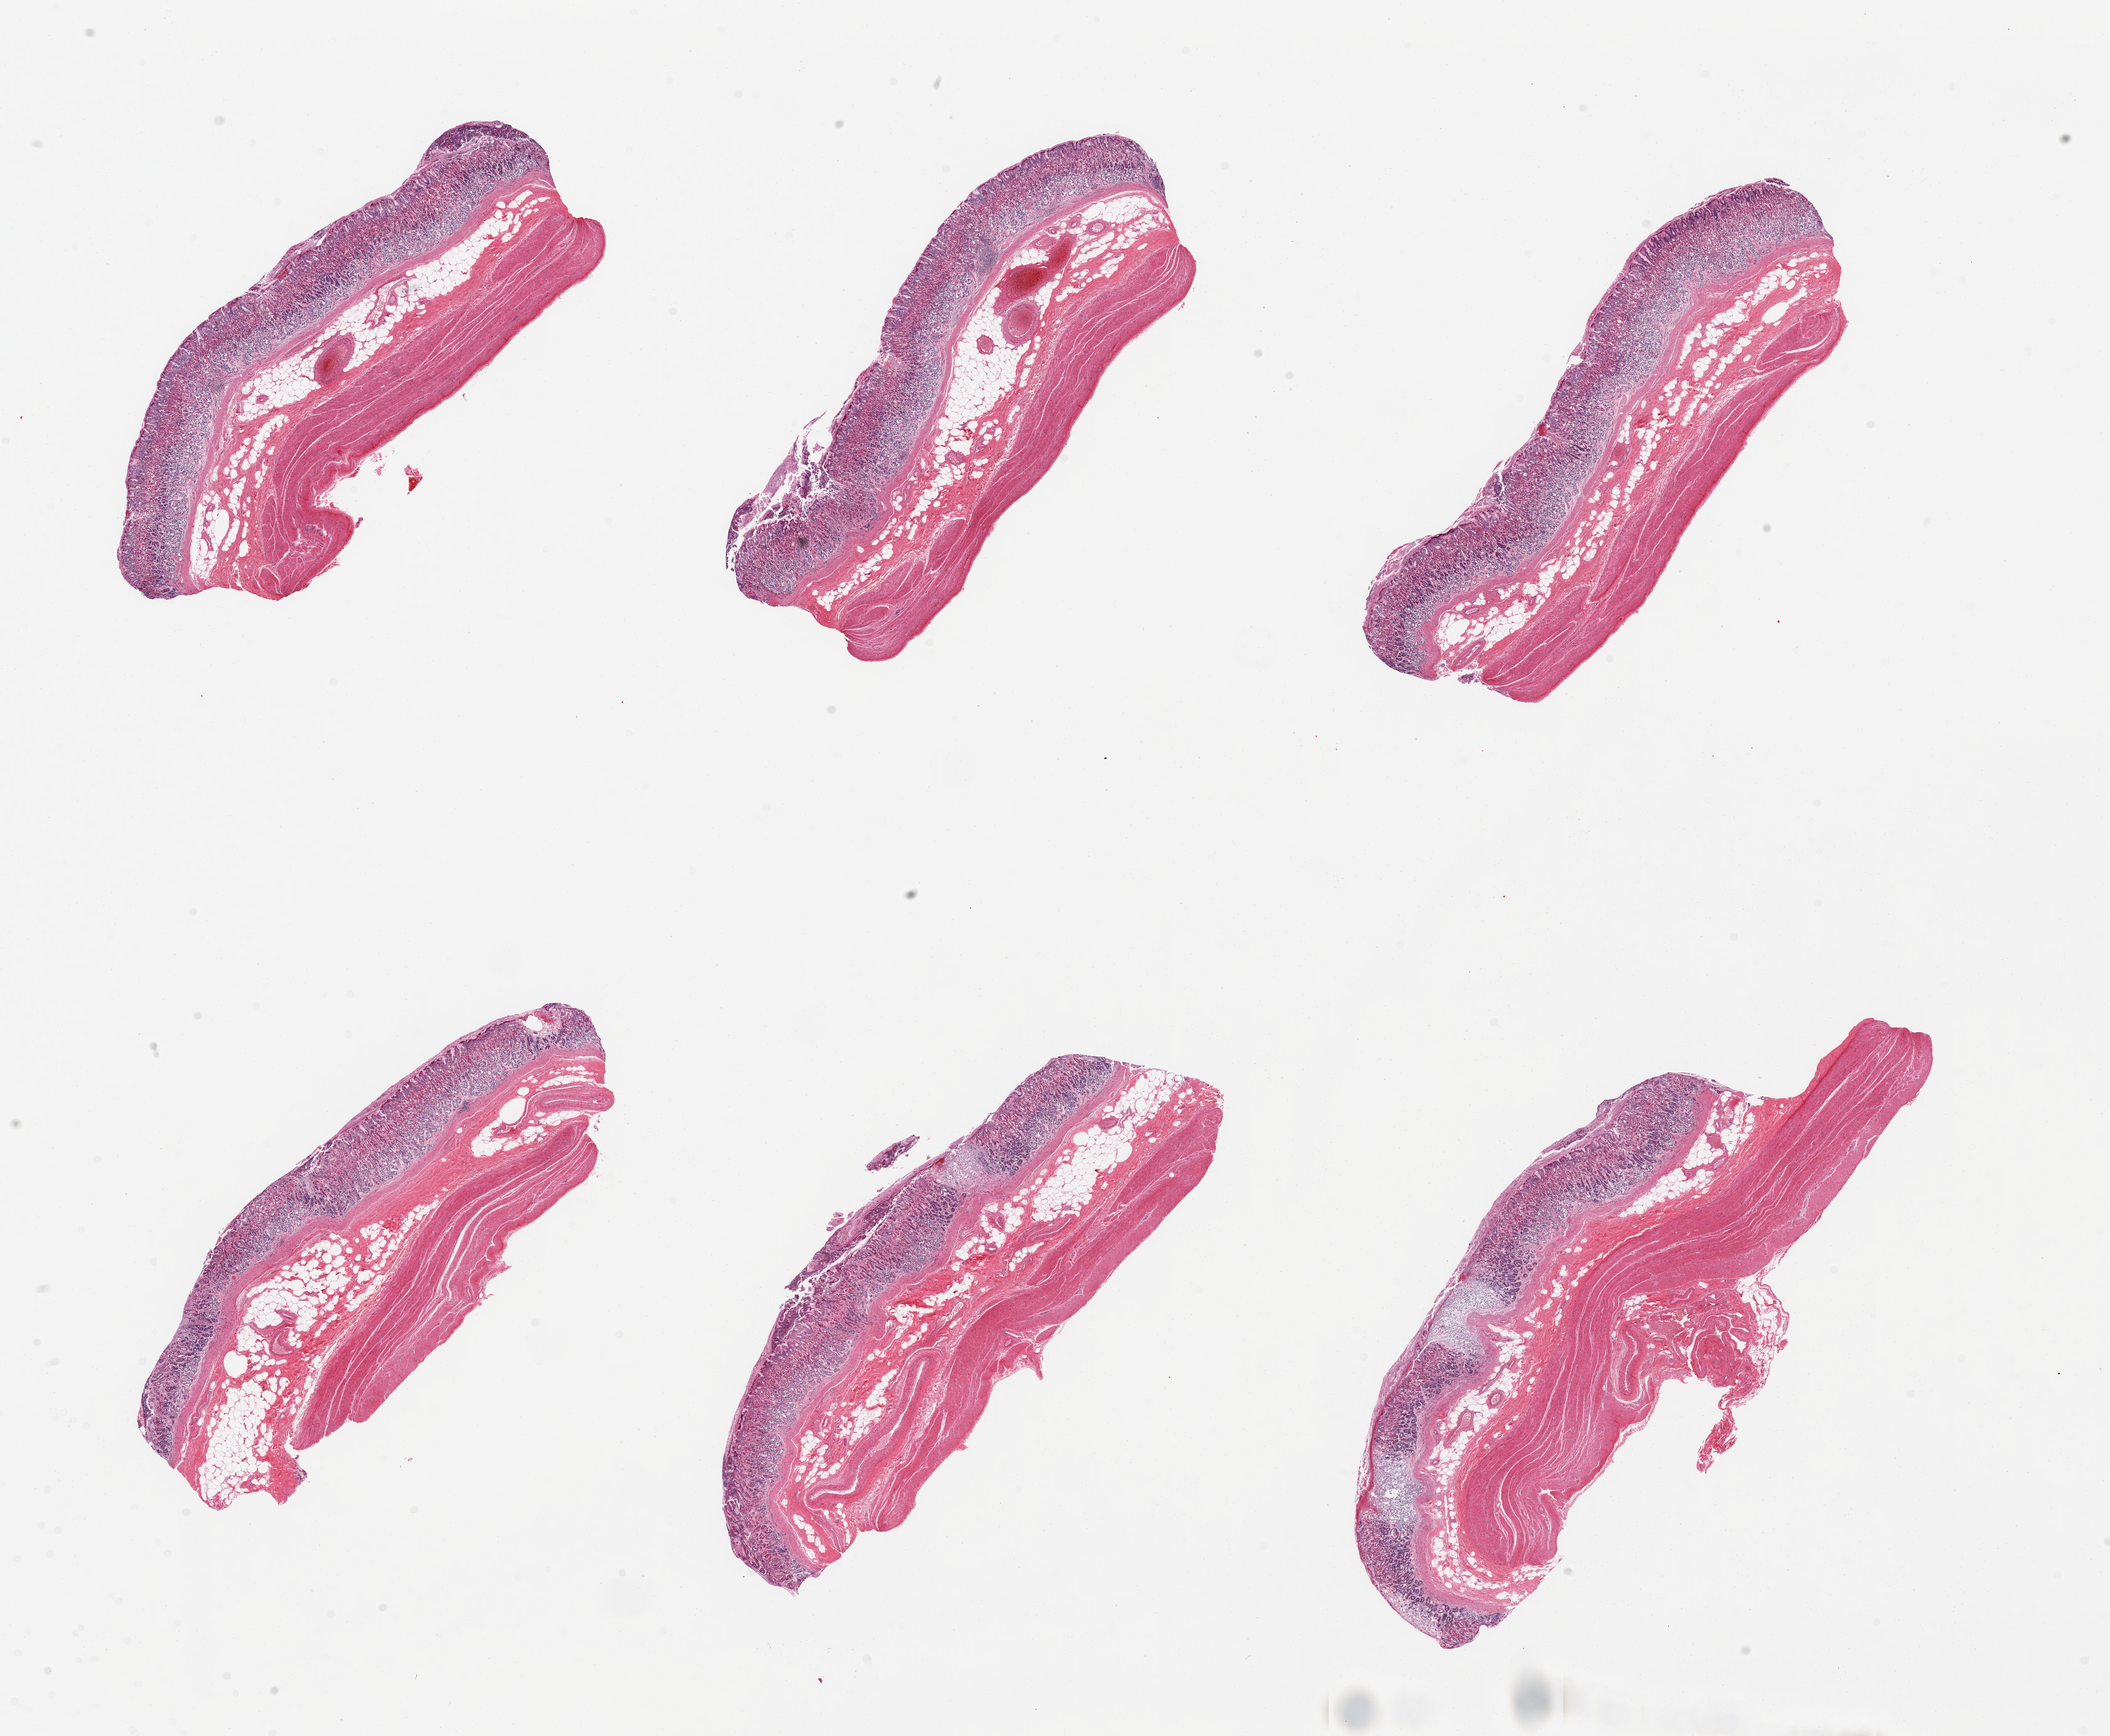
H&E whole-slide image, brightfield, whole scanned area (about 26.6 x 21.9 mm, acquisition: 20x scan) shown as a low-resolution overview, PAXgene-fixed, paraffin-embedded tissue, sampled site (target tissue): stomach, donor tissue sample.
Pathologist's review note for this sample: 6 pieces, mucosa up to ~1mm thick, ~30-40% thickness but moderately autolyzed.